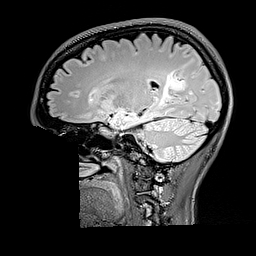
Brain MRI from a brain-tumour surgery series, one sagittal slice; slice 105 of 176 in the series (ordered by position); T2 FLAIR; 256 × 256 image matrix, field of view 256 × 256 mm. From the clinical record (not read from this slice): histopathology: Oligodendroglioma; WHO grade: 2; IDH mutation: yes.
Annotated regions visible in this slice (manually delineated by an expert):
- tumour: bounding box (x1, y1, x2, y2) in pixels: (160, 70, 186, 105)